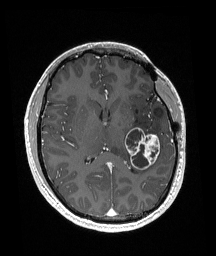
Brain MRI from a brain-tumour surgery series, one axial slice; position 87 of 192 along the scan axis; T1-weighted post-contrast; 1 mm slice thickness; 216 × 256 image matrix, field of view 211 × 250 mm. From the clinical record (not read from this slice): histopathology: Glioneuronal tumor; WHO grade: 2; tumour location: Left Superior Temporal Gyrus.
Annotated regions visible in this slice (expert manual segmentation):
- tumour: bounding box <125,127,160,170> (left, top, right, bottom; pixels)